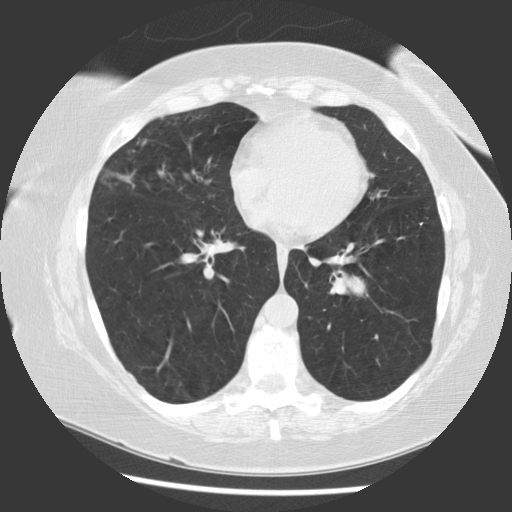
Low-dose screening chest CT, one axial slice. Position 58 of 130 along the scan axis. 120 kVp. Lung window (W 1500 / L -600 HU). 2.5 mm slice thickness. 512 × 512 image matrix, field of view 340 × 340 mm.
Annotated regions visible in this slice (manually delineated by an expert):
- lesion 1 (tumor, hilum of left lung): box from (x=342, y=276) to (x=365, y=295) px